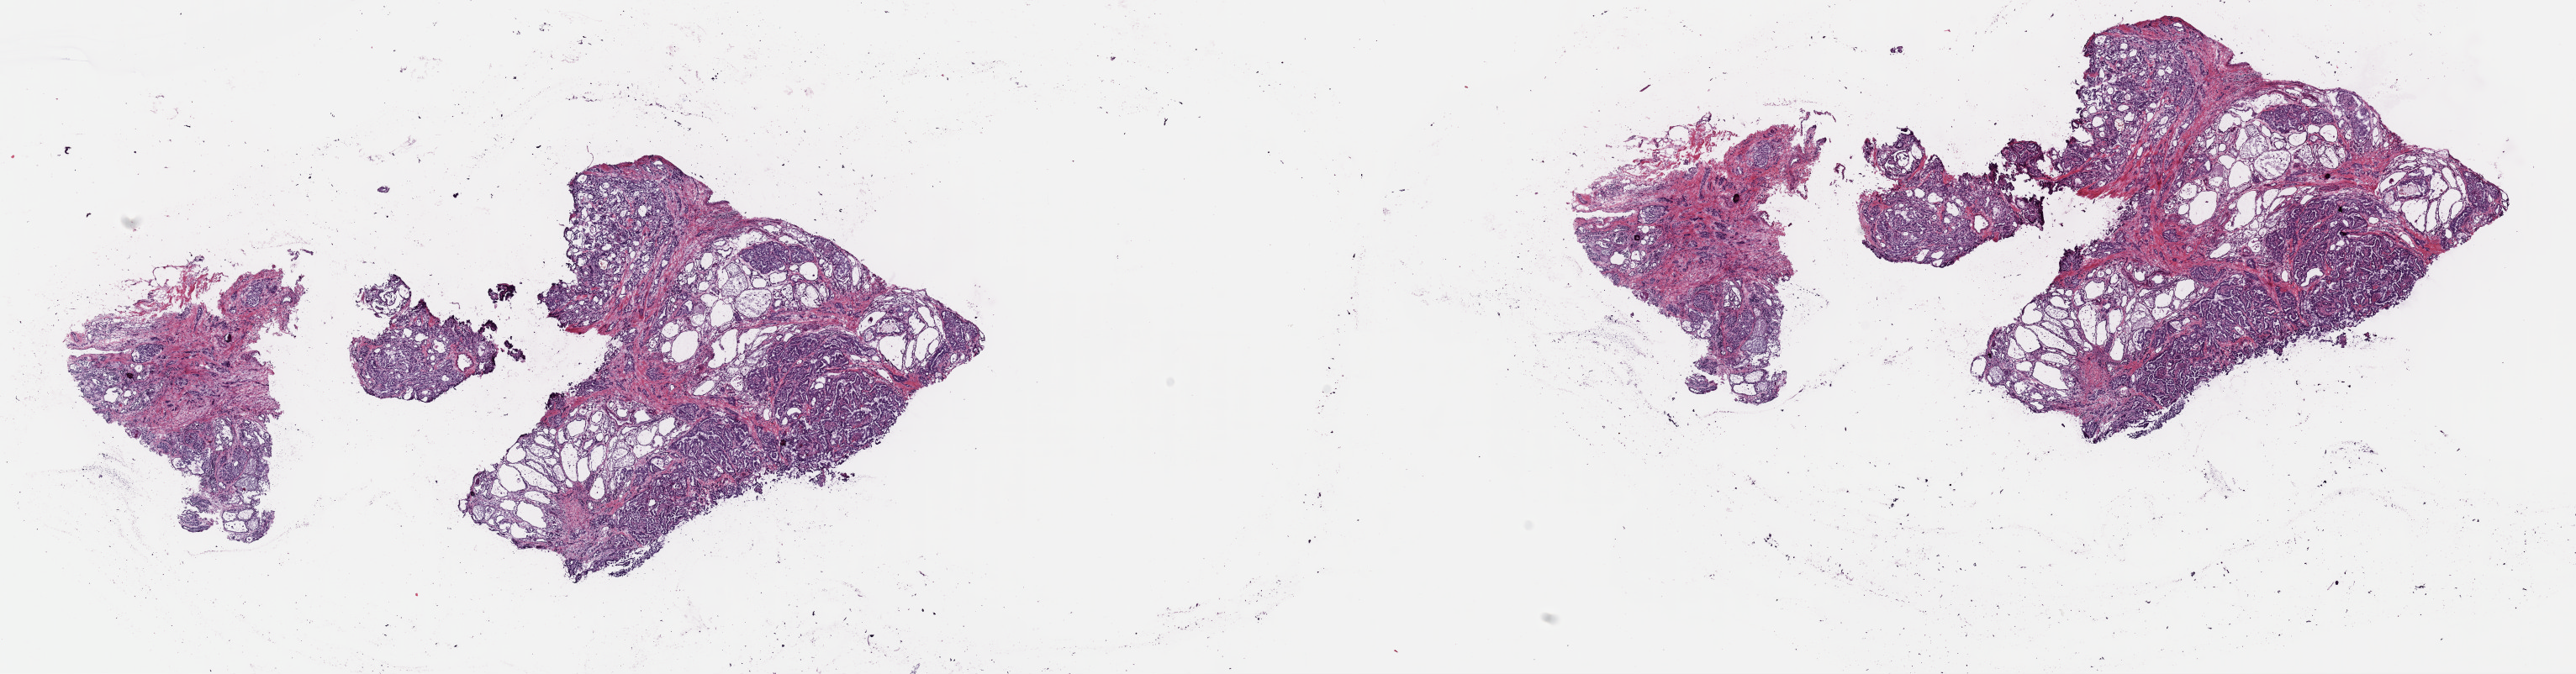
Whole-slide histology image, H&E — a low-resolution overview of the entire scanned area, about 24.2 x 6.3 mm; frozen section; metastatic tumour sample, sampled site not recorded. Female patient; age at initial diagnosis 51 years. Composition of this section per pathologist review: tumour cells 90%, tumour nuclei 95%, normal cells 0%, stromal cells 10%, necrosis 0%. Infiltration values recorded for this section: lymphocyte infiltration 2%, monocyte infiltration 1%, neutrophil infiltration 0%.
• this section: metastatic tumour tissue
• patient diagnosis: Papillary carcinoma, oxyphilic cell